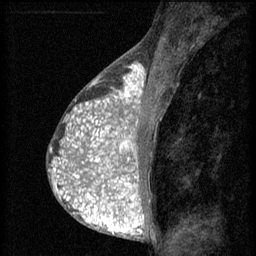
Breast MRI (dynamic contrast-enhanced), one sagittal slice; position 30 of 60 along the scan axis; 3 images stored at this slice position (order not interpretable as contrast timing); 1.5 T; TE 4.2 ms, TR 8.2 ms; 256 × 256 image matrix, field of view 180 × 180 mm. Female patient, age 38 years.
Structures marked on this image (semi-automatically segmented with operator editing):
- analysis volume of interest (the breast-tissue region the enhancement analysis was run in; not a lesion): bounding box [x1, y1, x2, y2] px = [92, 112, 152, 171]
- tumour enhancement mask (voxels above the 70 % enhancement threshold inside the analysis volume of interest): [92, 112, 140, 171]